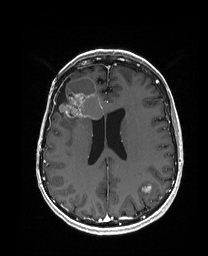
Brain MRI from a brain-tumour surgery series, one axial slice. Position 74 of 192 along the scan axis. T1-weighted post-contrast. 1 mm slice thickness. 208 × 256 image matrix, field of view 203 × 250 mm. Case-level facts recorded for this patient, not image findings: histopathology: Metastatic Carcinoma from Breast primary; tumour location: Right Frontal.
Annotated regions visible in this slice (outlined manually by an expert reader):
- previous resection cavity: box from (x=54, y=78) to (x=70, y=111) px
- tumour: (x=55, y=77)–(x=104, y=128)